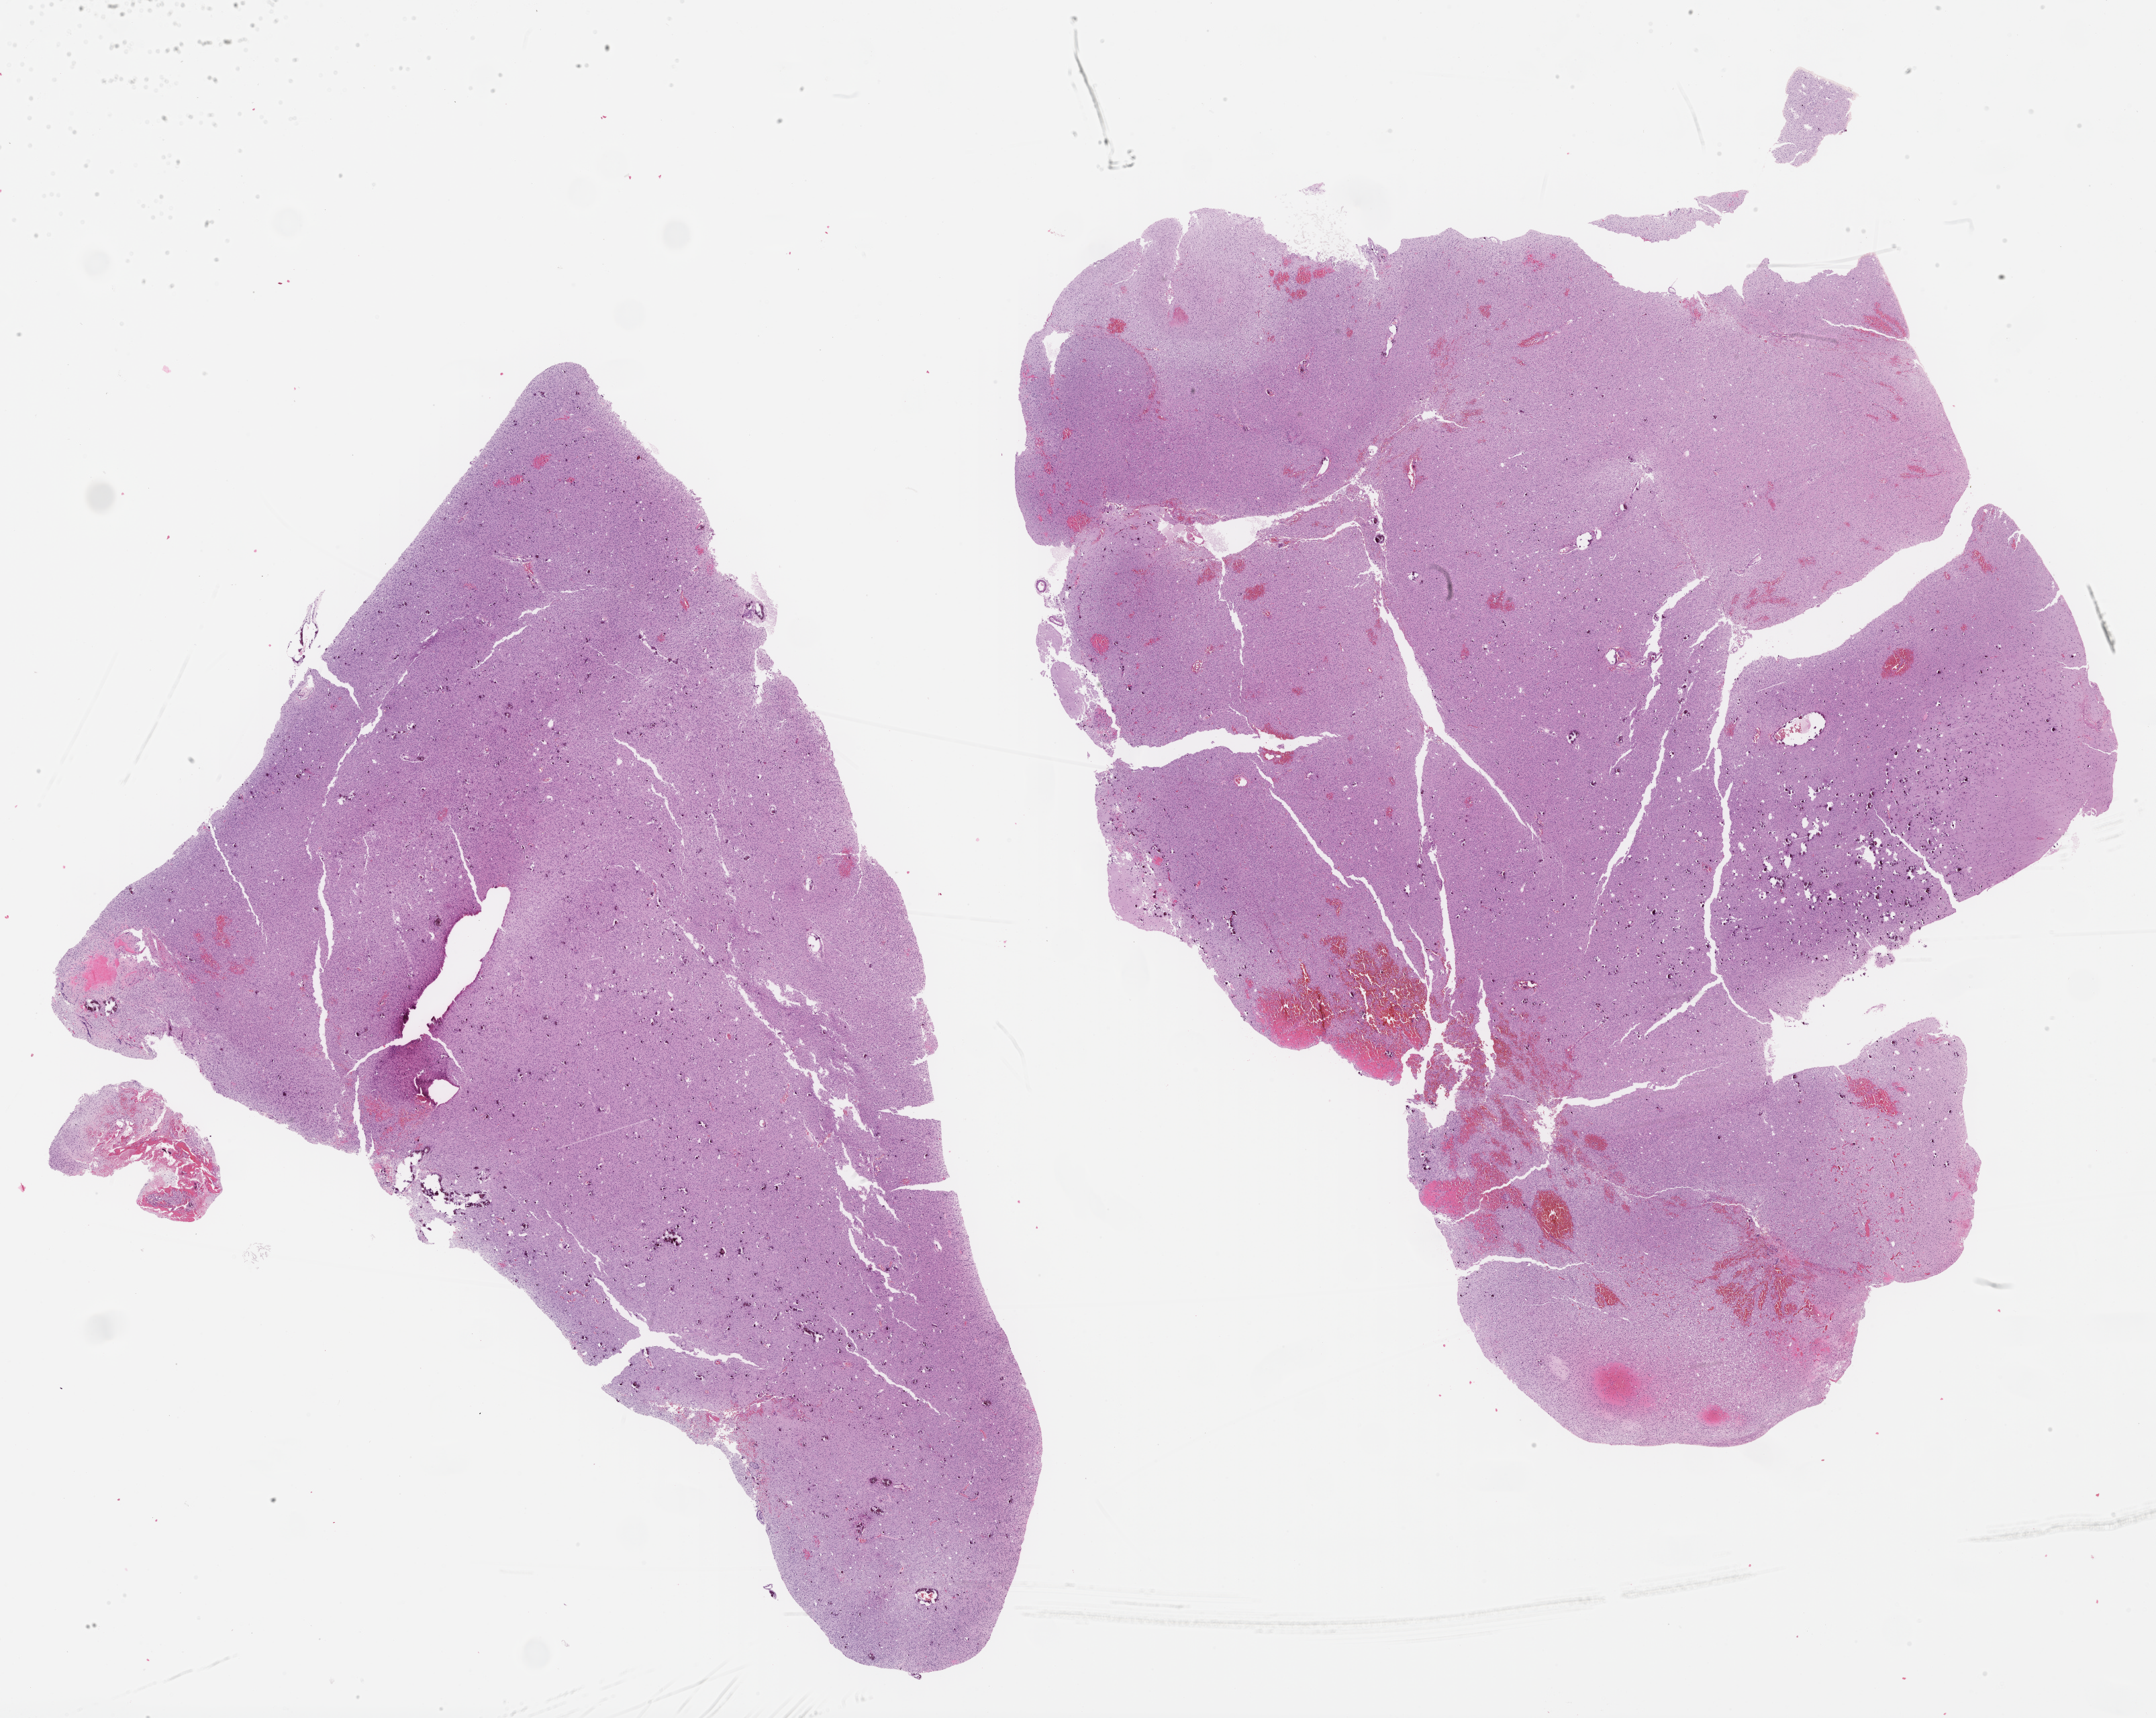
Digitized H&E tissue section (whole slide), low-resolution overview of the scanned area, about 25.9 x 20.6 mm. Formalin-fixed paraffin-embedded (FFPE) diagnostic section. Brain, primary tumour sample. Female, age 53 years at initial diagnosis. Histologic grade: G2 (moderately differentiated).
- laterality: right
- diagnosis: Oligodendroglioma, NOS